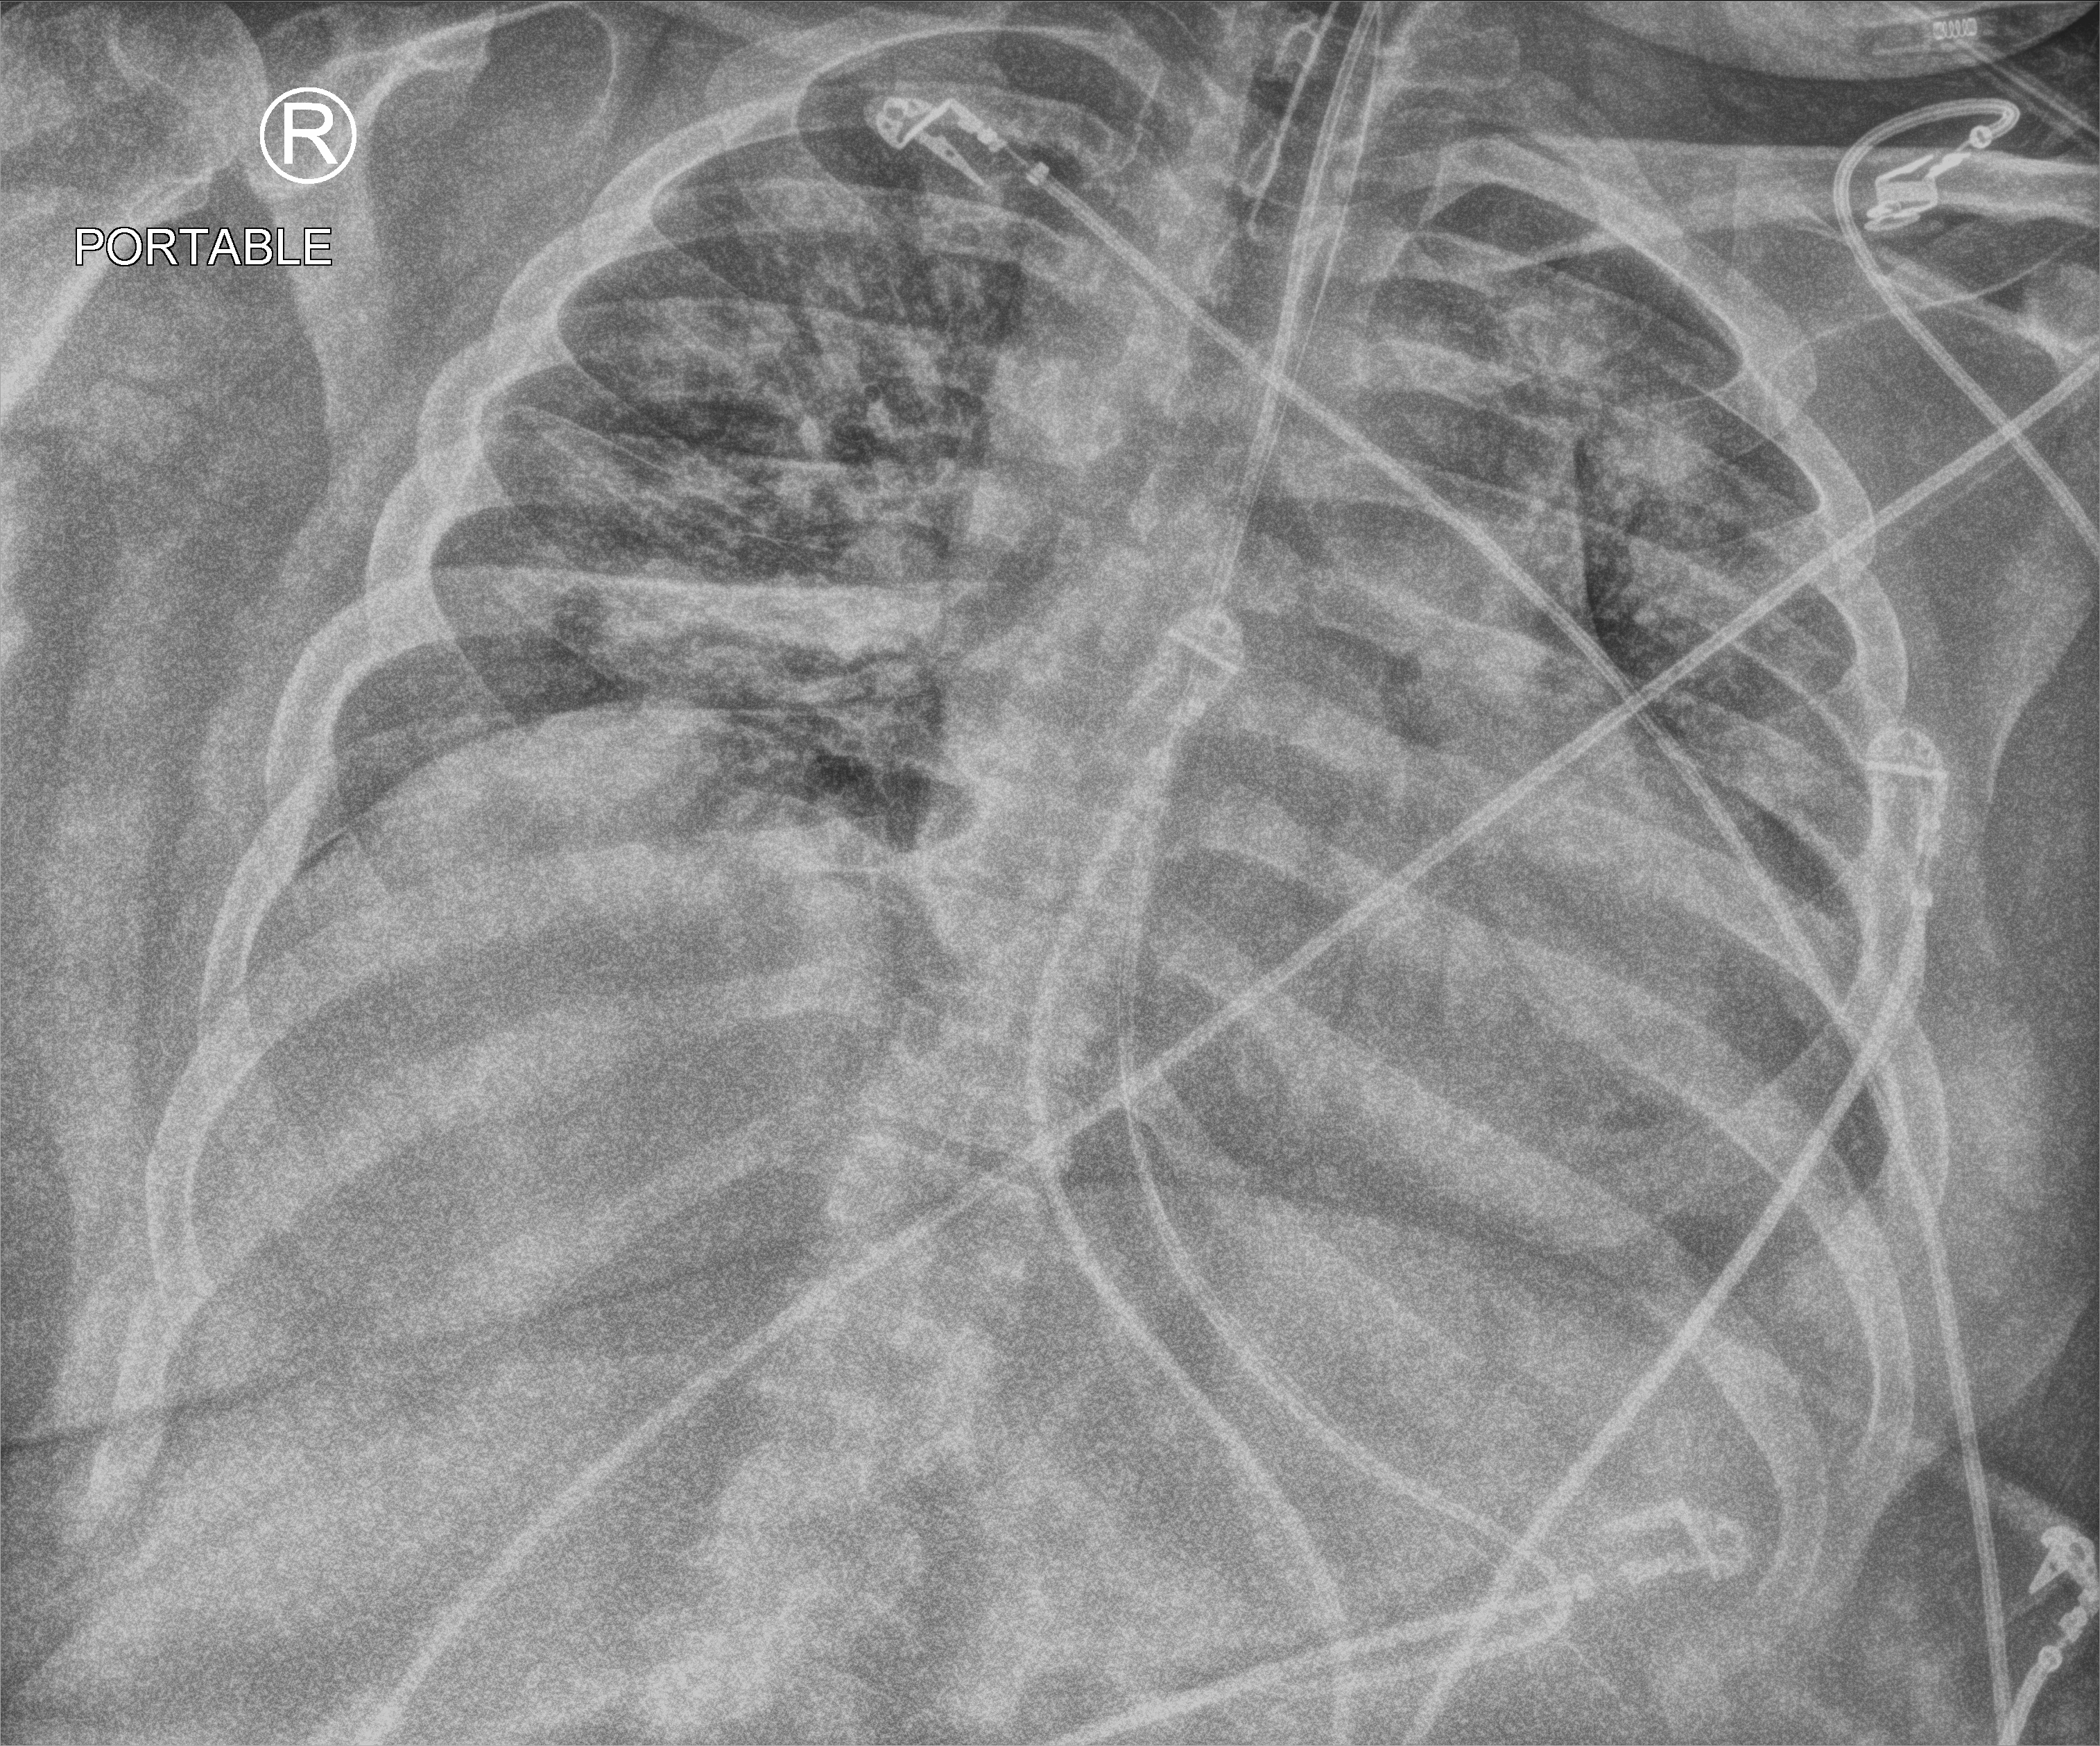
Chest X-ray (portable), anteroposterior (AP) projection. Adult patient hospitalised with COVID-19, age 18–59 years.
Admission-level facts for this patient (not findings on this image; timing relative to this image not recorded):
- admitted to intensive care during this hospital stay: yes